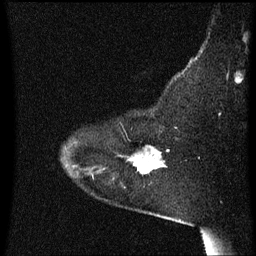
Breast MRI (dynamic contrast-enhanced), one sagittal slice. Position 47 of 60 along the scan axis. Dynamic contrast-enhanced series, image 2 of 3 at this slice position (ordered by acquisition). 1.5 T. TE 4.2 ms, TR 8.4 ms. 2 mm slice thickness. 256 × 256 image matrix, field of view 200 × 200 mm. Female patient, age 54 years. From the clinical record (not read from this slice): setting: breast cancer imaged before/during neoadjuvant chemotherapy; receptor status: HR-positive, HER2-negative.
Annotated regions visible in this slice (semi-automatically segmented with operator editing):
- analysis volume of interest (the breast-tissue region the enhancement analysis was run in; not a lesion): box from (x=123, y=152) to (x=167, y=185) px
- tumour enhancement mask (voxels above the 70 % enhancement threshold inside the analysis volume of interest): (x=134, y=152)–(x=166, y=173)